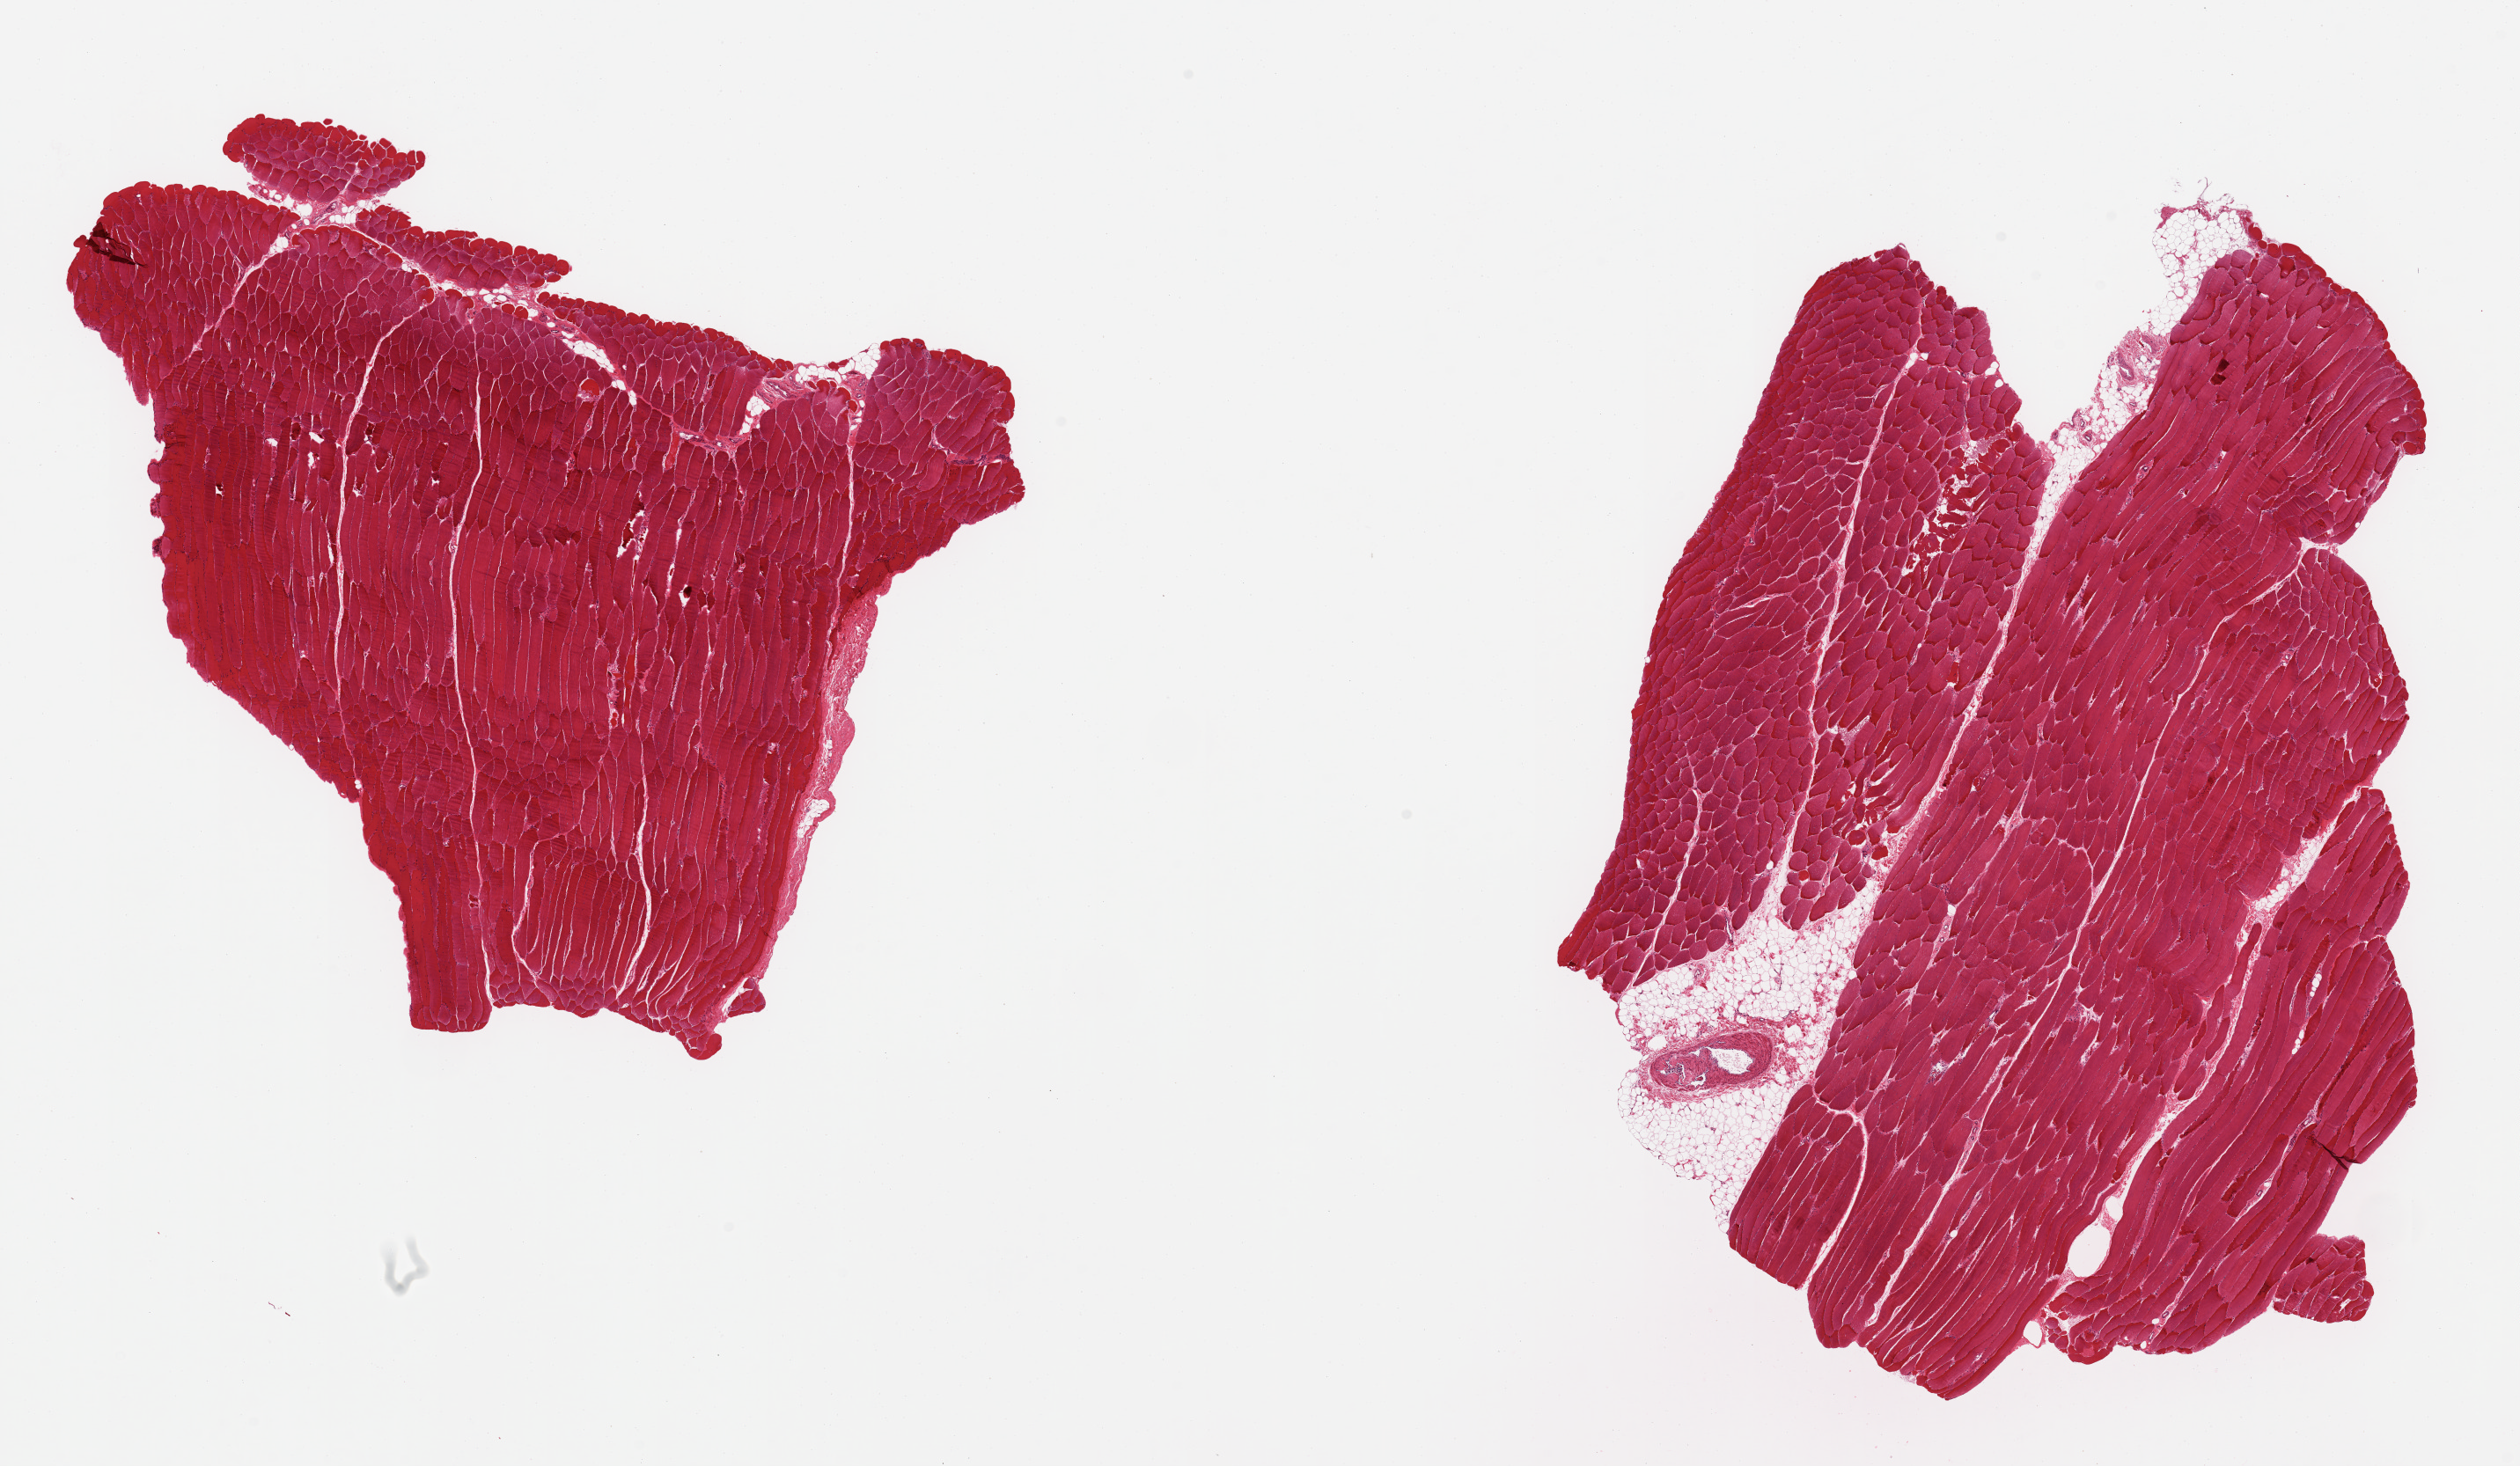
Whole-slide image, hematoxylin and eosin (H&E) stain, brightfield, low-resolution overview of the scanned area, about 22.6 x 13.2 mm. PAXgene-fixed paraffin-embedded (PFPE) section. Target tissue: skeletal muscle. Donor tissue sample. Donor sex: male.
Reviewer comment on this tissue sample: 2 pieces; 1 has 10% internal fat.